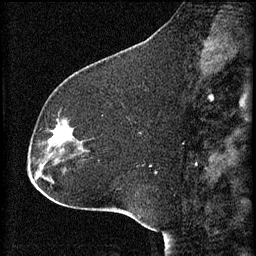
Breast MRI (dynamic contrast-enhanced), one sagittal slice. Slice 22 of 60 in the series (ordered by position). 3 images stored at this slice position (order not interpretable as contrast timing). 1.5 T. TE 4.2 ms, TR 8.2 ms. 2 mm slice thickness. 256 × 256 image matrix, field of view 180 × 180 mm. Patient: female, 32 years.
Structures marked on this image (semi-automatic segmentation, software-assisted and operator-edited):
- analysis volume of interest (the breast-tissue region the enhancement analysis was run in; not a lesion): bounding box <48,114,84,157> (left, top, right, bottom; pixels)
- tumour enhancement mask (voxels above the 70 % enhancement threshold inside the analysis volume of interest): <52,130,63,145>